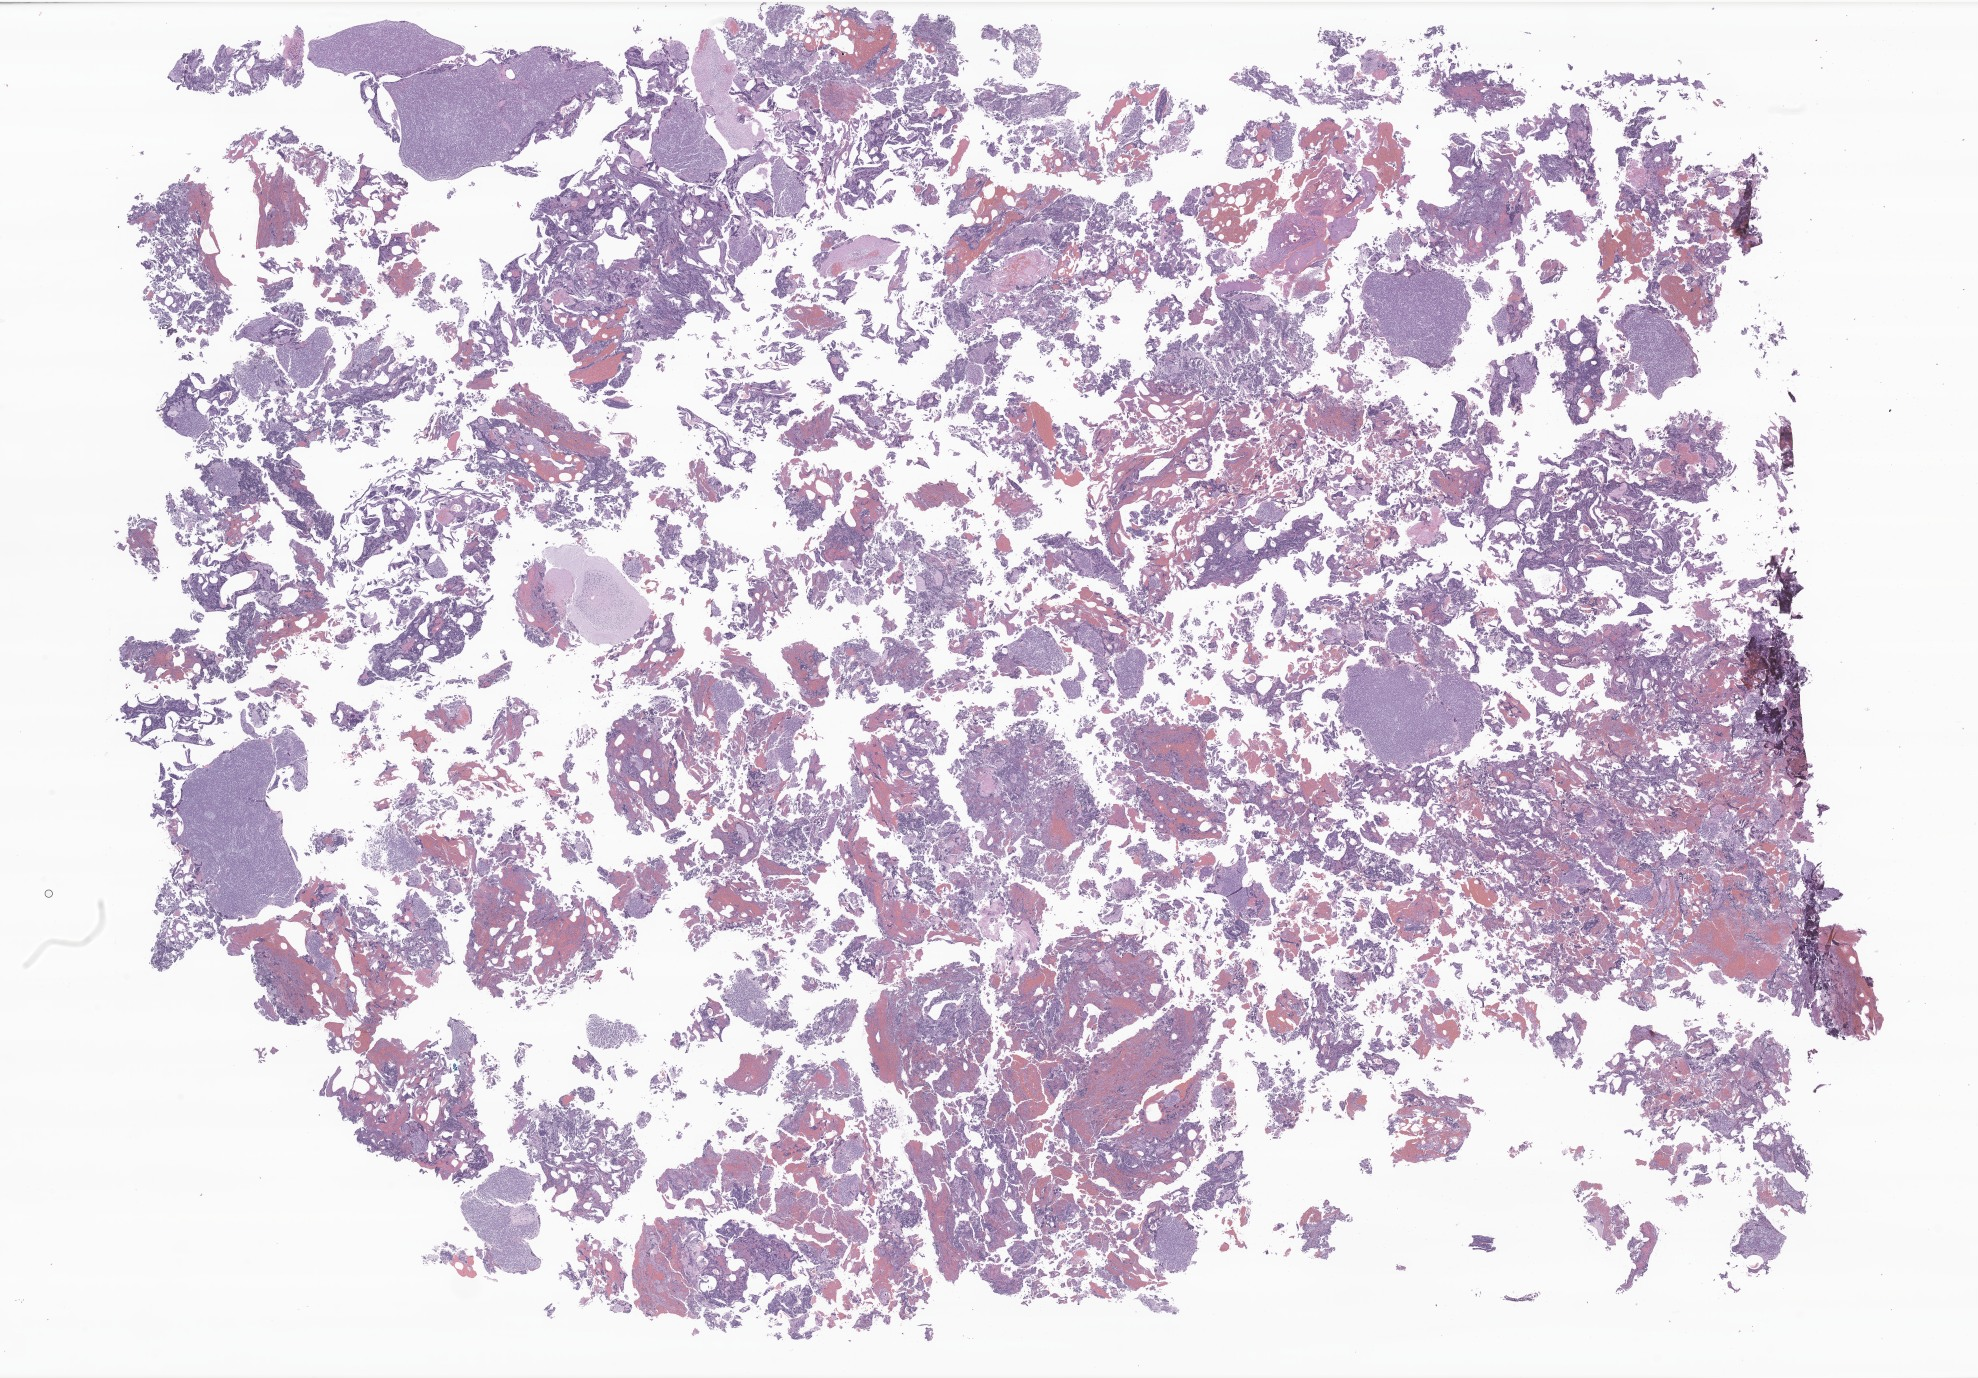
Haematoxylin and eosin whole-slide image of tumor tissue from the brain — low-resolution overview of the scanned area, about 33.4 x 23.2 mm, formalin-fixed paraffin-embedded section. Patient: female, age 169 months (14 years 1 month).
Diagnosis: Medulloblastoma, NOS.